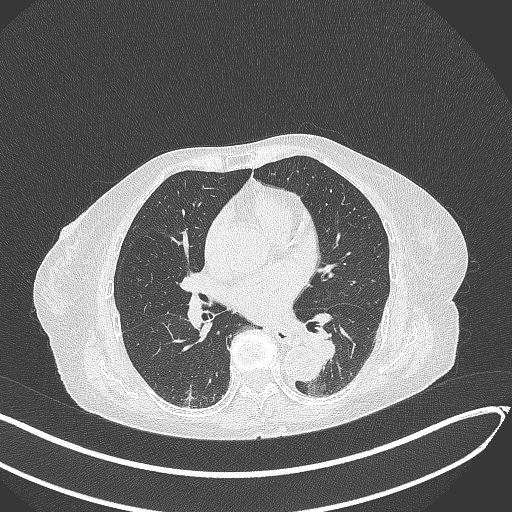
Chest CT, one axial slice; slice 122 of 324 in the series (ordered by position); reconstruction kernel B70f; 120 kVp; lung window (W 1500 / L -600 HU); 512 × 512 image matrix, field of view 400 × 400 mm. Patient: female, 82 years. Case-level facts recorded for this patient, not image findings: clinical TNM (as recorded): T1b N0 M1.
Outlined on this slice (rectangle marked by the reading radiologist):
- lung tumour (recorded histology: adenocarcinoma): box from (x=300, y=324) to (x=340, y=364) px